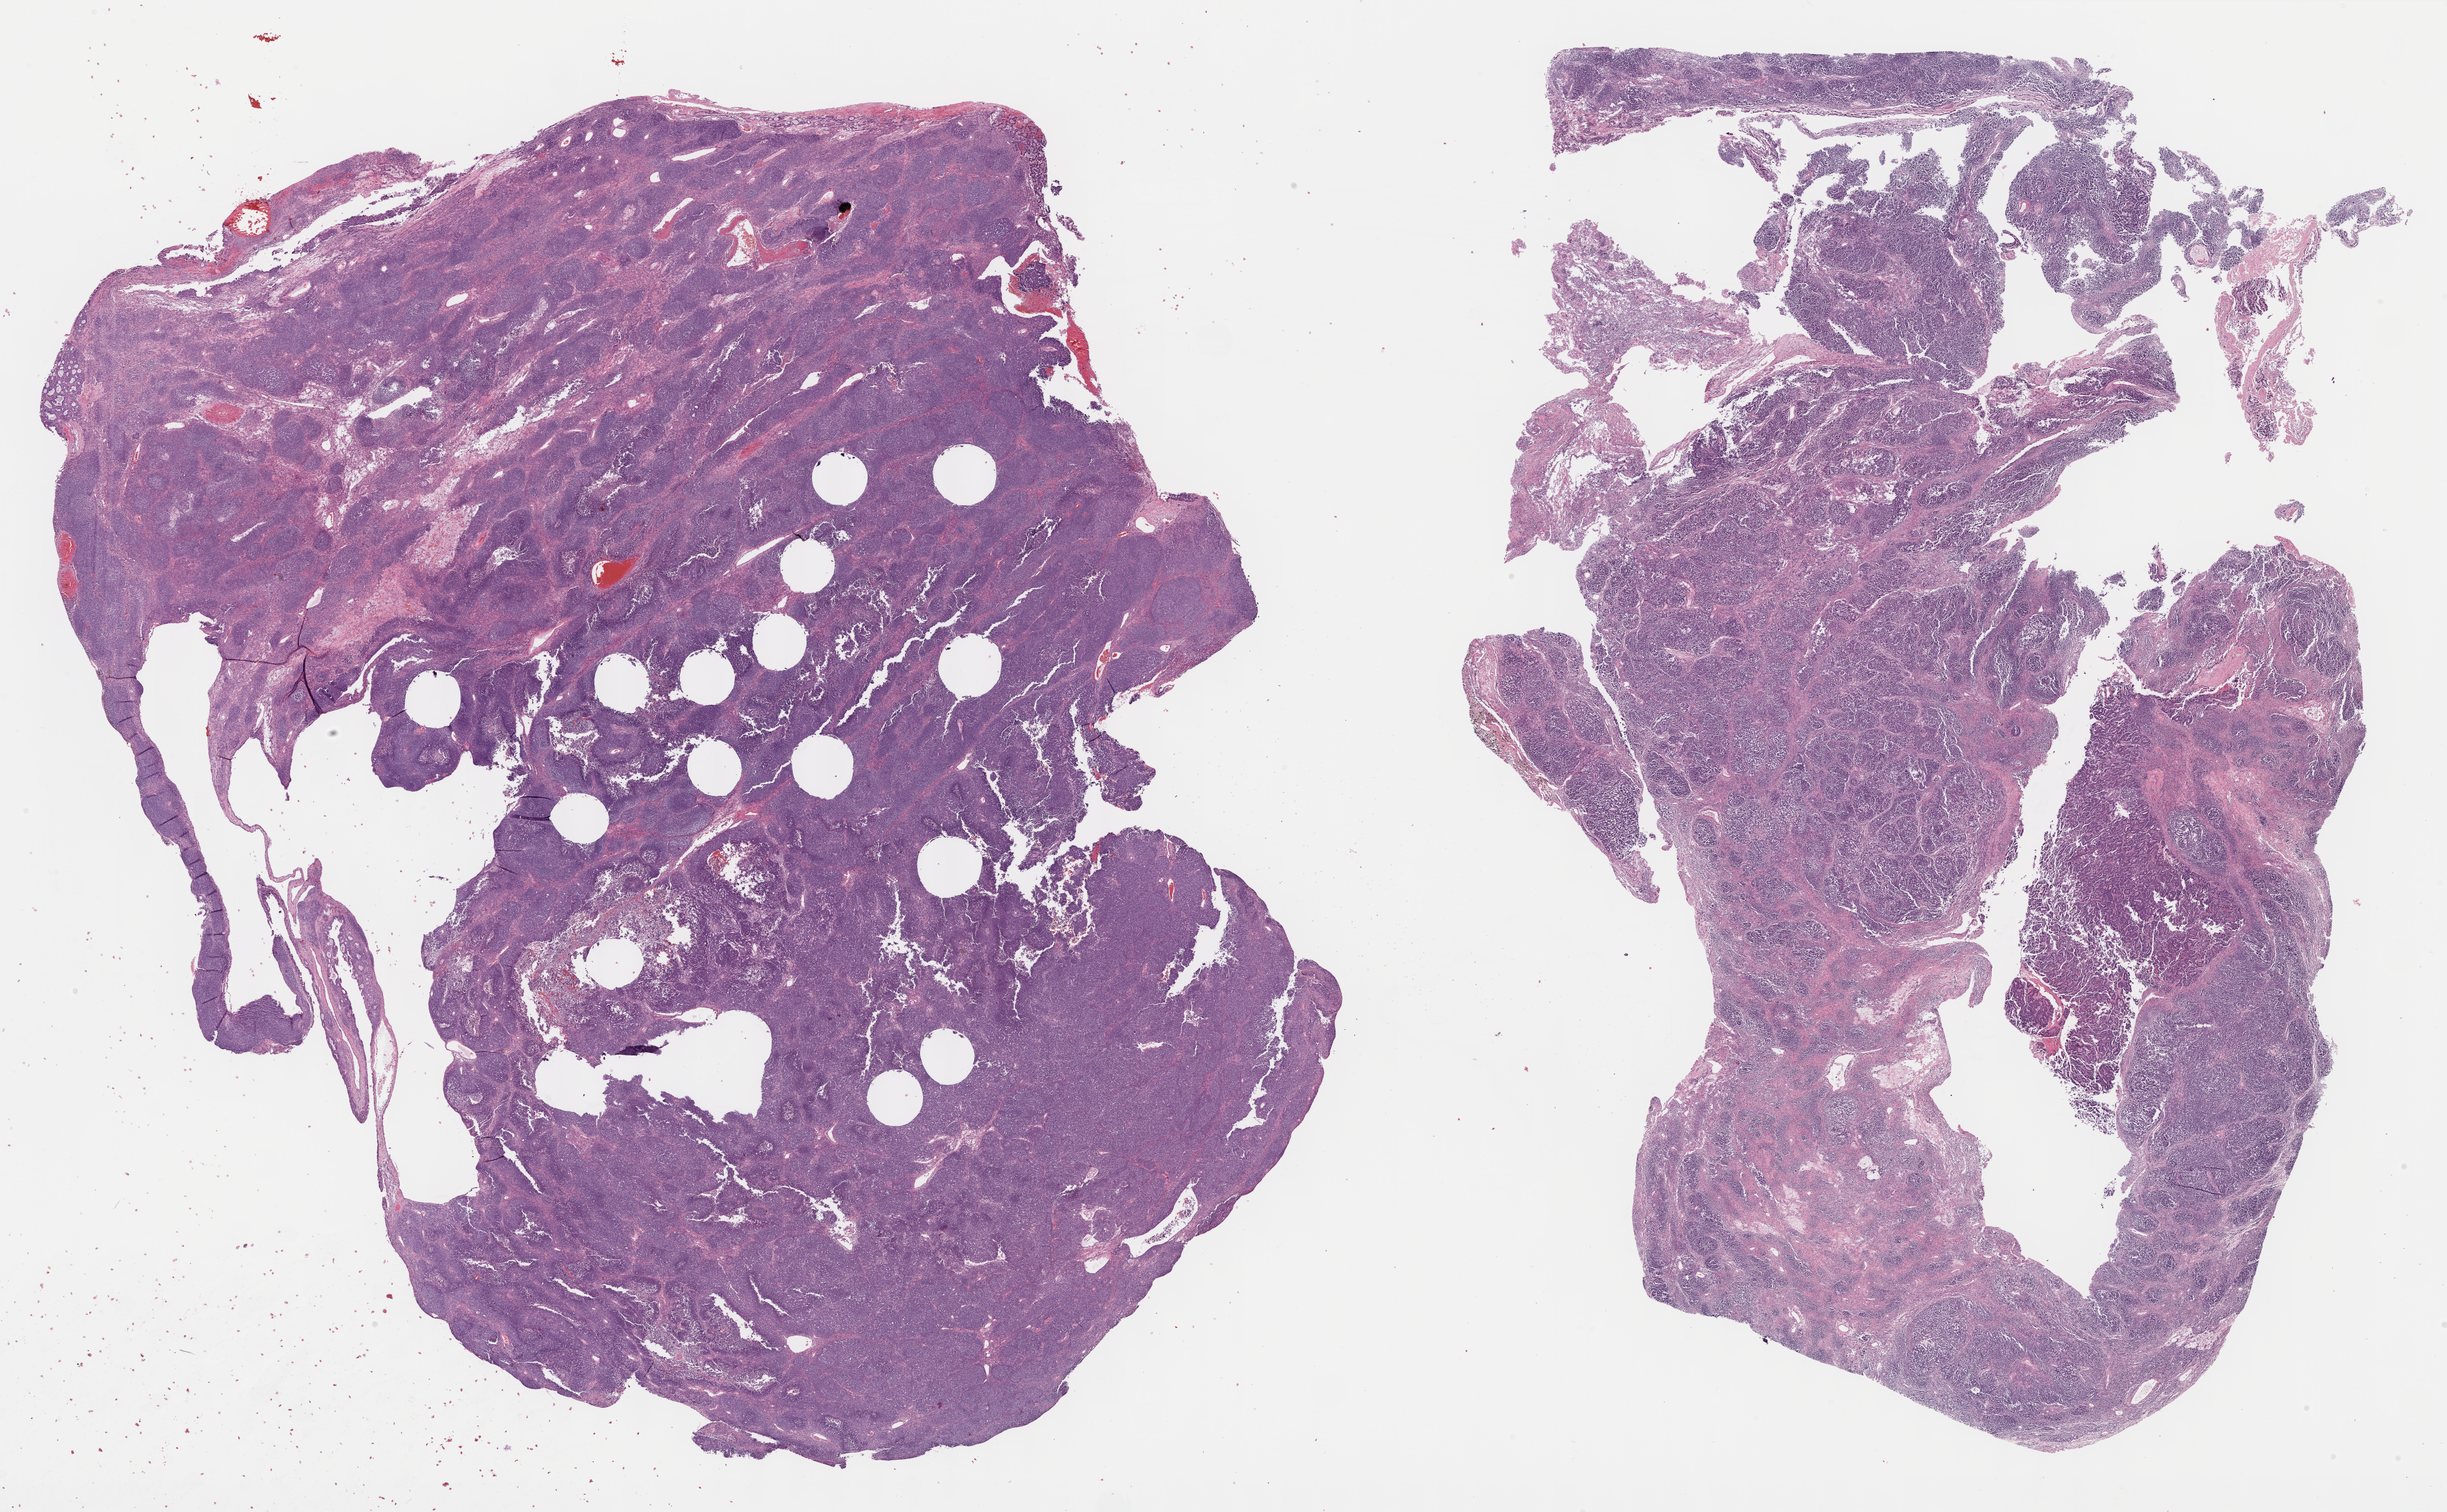
Whole-slide histology image, H&E-stained, low-resolution overview of the scanned area, about 31.7 x 19.6 mm (from a 40x scan); formalin-fixed paraffin-embedded (FFPE) diagnostic section; ovary, primary tumour sample. Patient: female, age at initial diagnosis 55 years. Histologic grade: G3 (poorly differentiated).
Pathologic diagnosis: Serous cystadenocarcinoma, NOS. FIGO stage: IIIC.